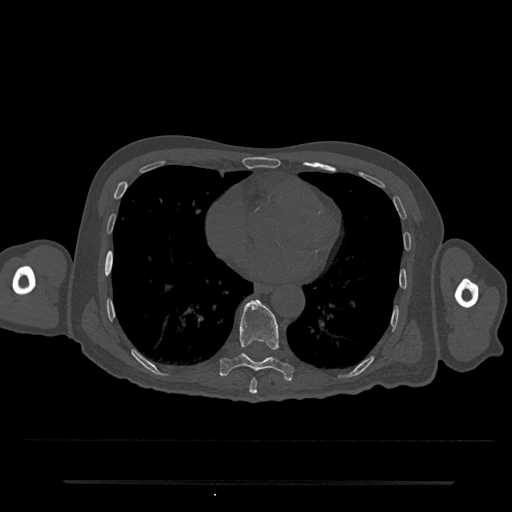
CT including the spine, one axial slice. Position 370 of 797 along the scan axis. Reconstruction kernel Br40s/3. Bone window (W 1800 / L 400 HU). 0.5 mm slice thickness. 512 × 512 image matrix, field of view 427 × 427 mm. Male patient, age 74 years. From the clinical record (not read from this slice): primary cancer: prostate.
Annotated regions visible in this slice (semi-automatically segmented with operator editing):
- T8 vertebra: bounding box <249,378,258,394> (left, top, right, bottom; pixels)
- T9 vertebra: <219,299,294,380>